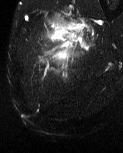
MRI of an extremity soft-tissue mass, one axial slice. Position 11 of 60 along the scan axis. T2-weighted fat-saturated. MR volume resampled by the dataset authors to the PET/CT grid (not the native acquisition matrix). 3.27 mm slice thickness. 123 × 153 image matrix, field of view 120 × 149 mm. Male patient. From the clinical record (not read from this slice): histological type: pleiomorphic liposarcoma; grade: high; site of the primary tumour: left thigh.
Outlined on this slice (expert contour drawn on MRI and transferred to this co-registered scan by the dataset authors):
- gross tumour volume including surrounding oedema: bounding box <45,13,94,62> (left, top, right, bottom; pixels)